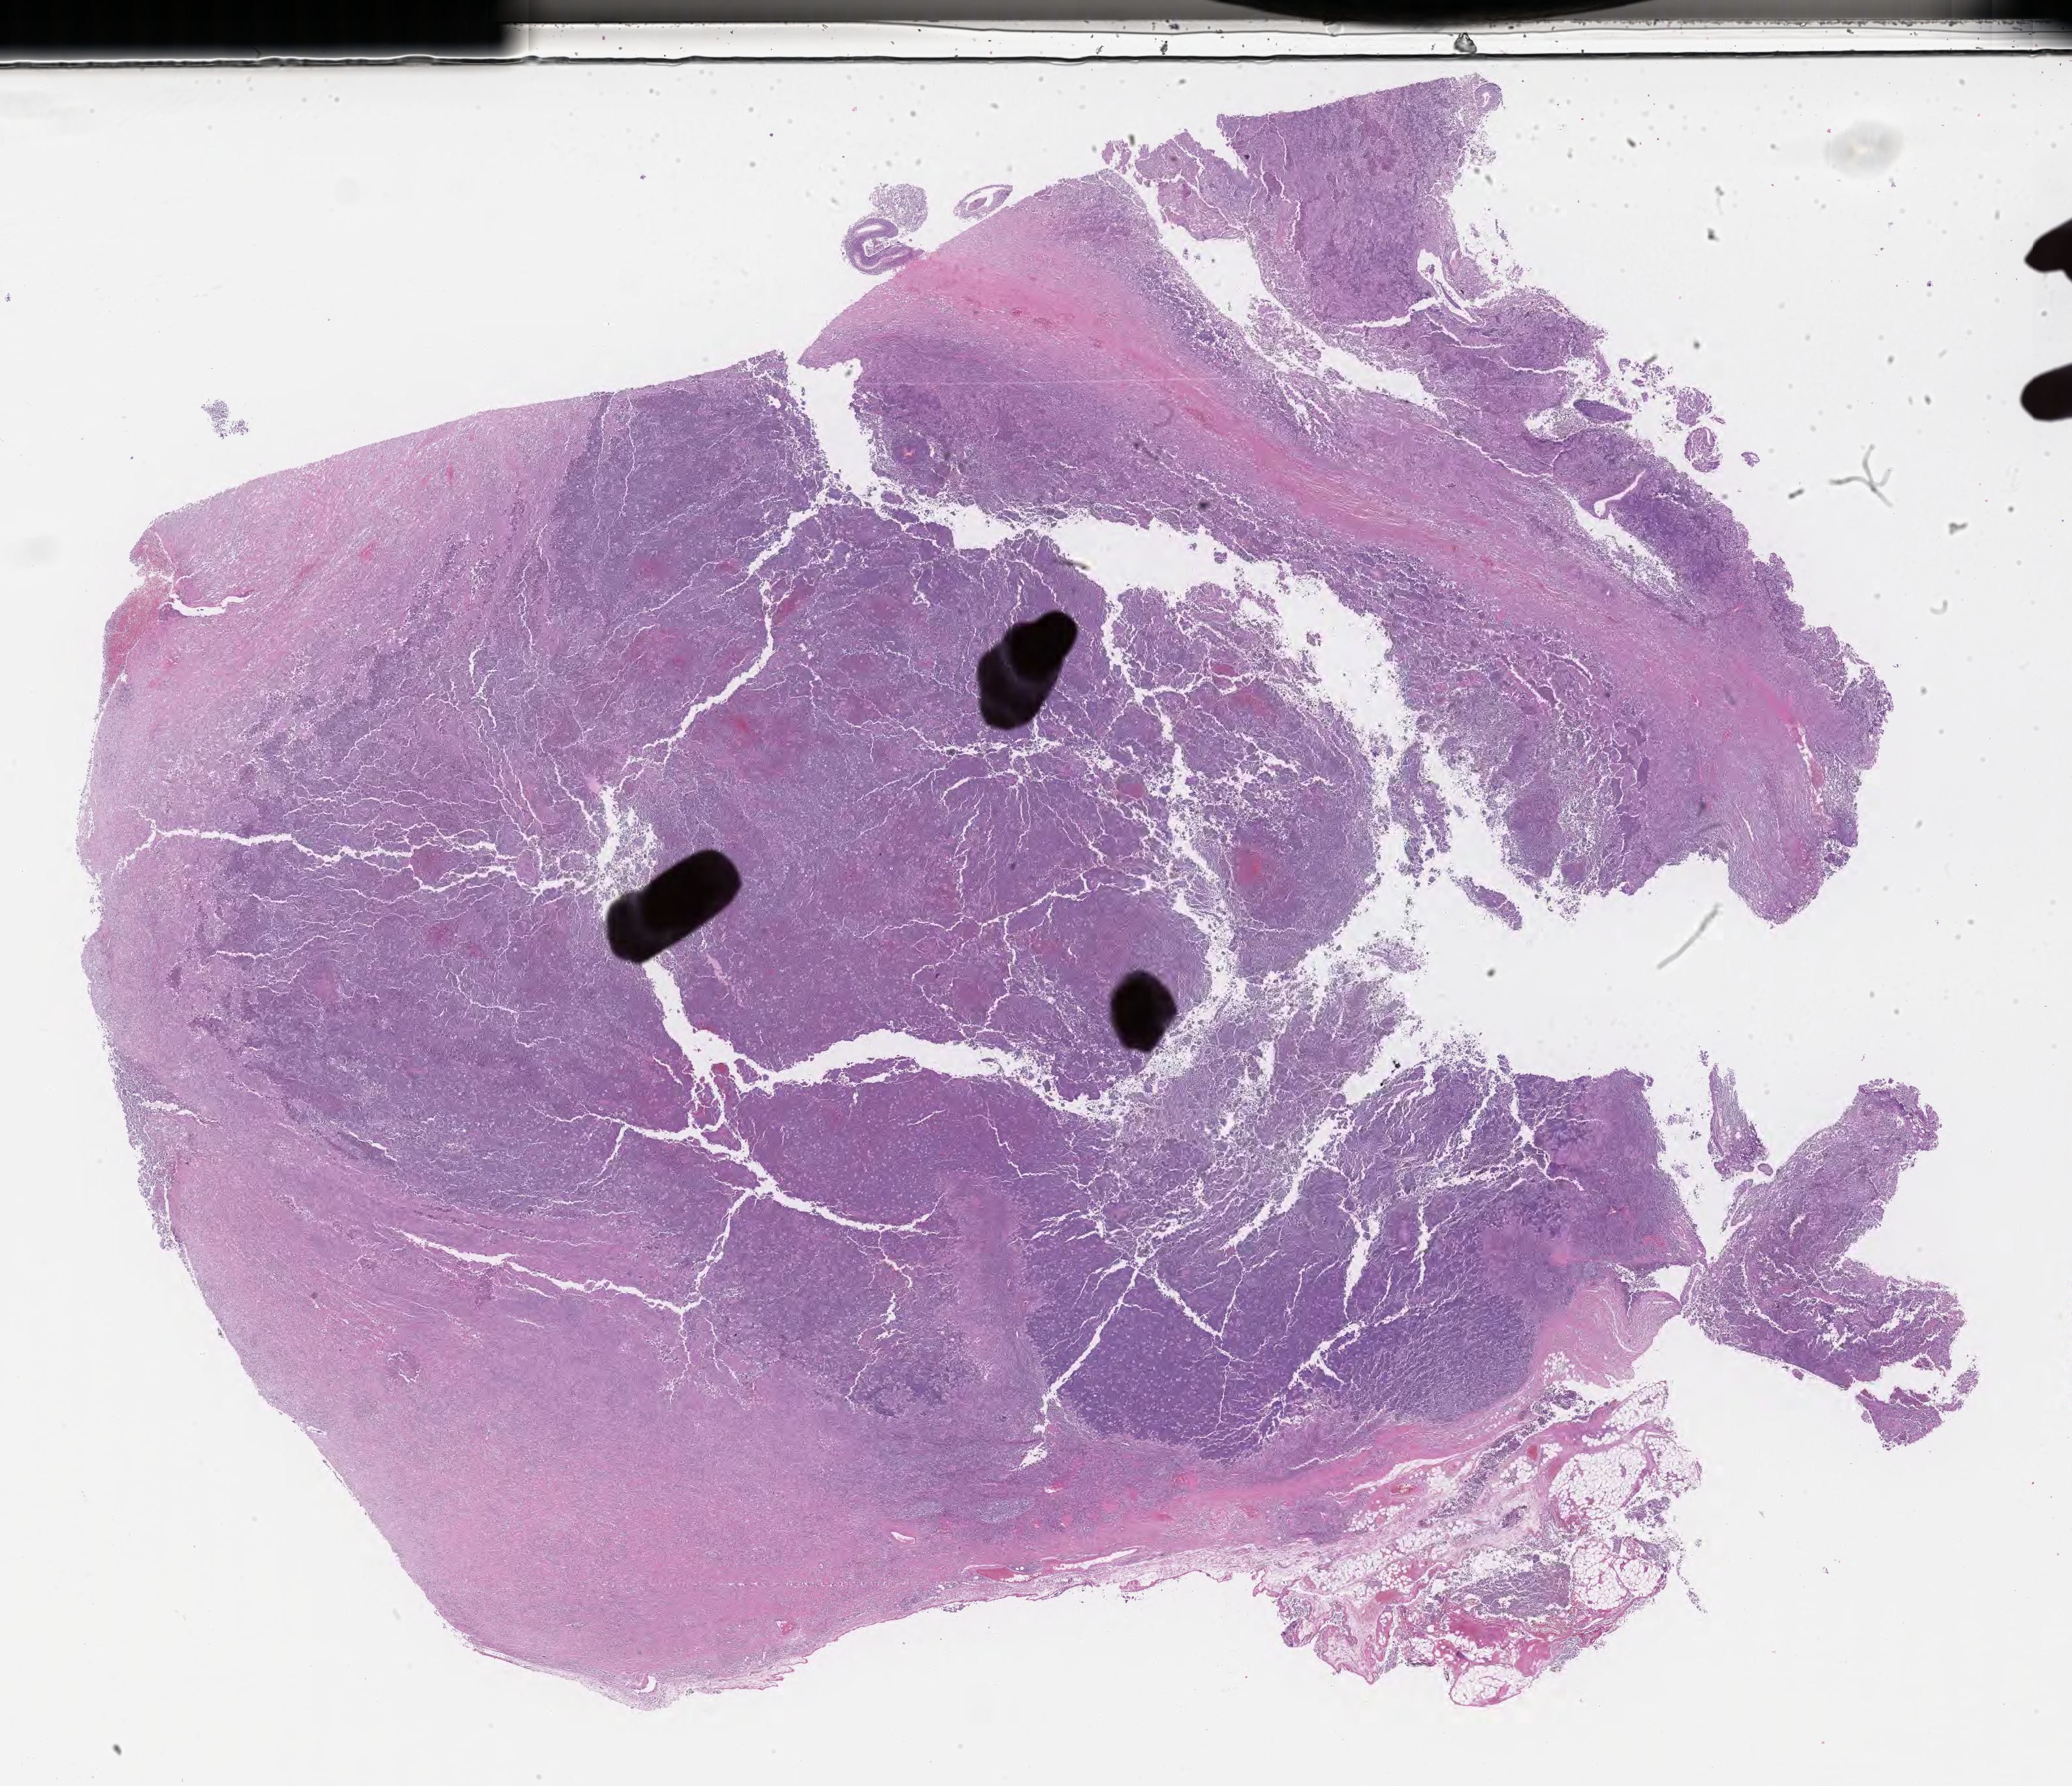
Haematoxylin and eosin whole-slide image — a low-resolution overview of the entire scanned area, about 25.7 x 22.1 mm; tumor tissue. Patient: female, aged 74.
- diagnosis: Burkitt lymphoma, NOS